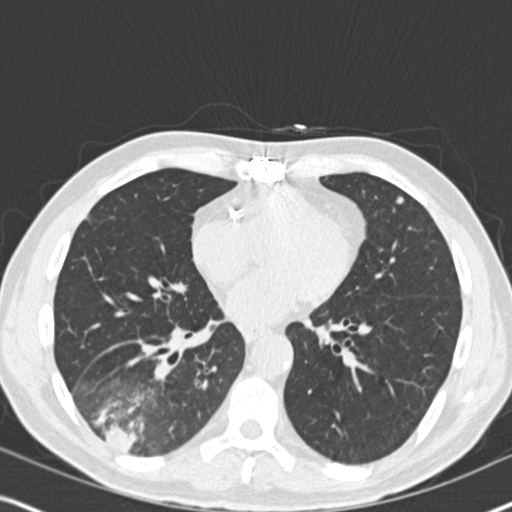
Low-dose screening chest CT, one axial slice. Position 84 of 182 along the scan axis. Lung window (W 1500 / L -600 HU). 512 × 512 image matrix, field of view 330 × 330 mm.
Outlined on this slice (manually delineated by an expert):
- lesion 1 (tumor, lower lobe of right lung): bounding box (x1, y1, x2, y2) in pixels: (101, 423, 139, 452)